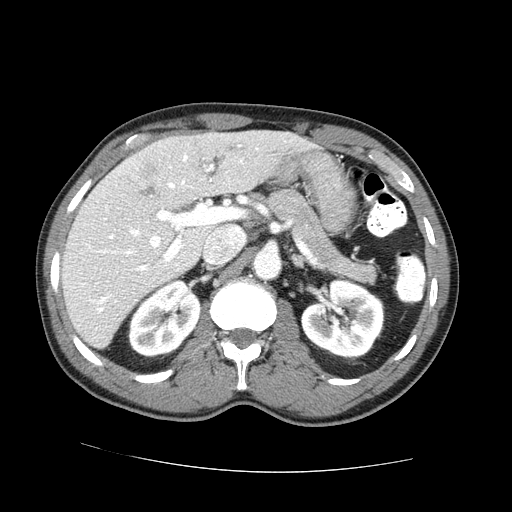
Contrast-enhanced abdominal CT (liver protocol), one axial slice; position 41 of 73 along the scan axis; one of 2 acquisitions stored at this slice position; soft-tissue window (W 400 / L 40 HU); 512 × 512 image matrix, field of view 380 × 380 mm. From the clinical record (not read from this slice): diagnosis: hepatocellular carcinoma (patient treated with transarterial chemoembolisation; whether this scan precedes or follows treatment is not stated here); TNM stage (as recorded): Stage-IVA; Child-Pugh class: A; tumour differentiation: no biopsy; tumour nodularity: uninodular.
Annotated regions visible in this slice (semi-automatic segmentation, software-assisted and operator-edited):
- liver parenchyma outside the tumour (the mass and vessels are separate outlines, so this box may not span the whole liver): bounding box [x1, y1, x2, y2] px = [60, 130, 312, 348]
- mass: [139, 159, 156, 196]
- liver vessels: [88, 145, 258, 312]